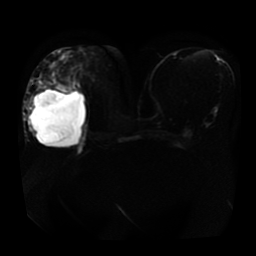
Breast MRI, one axial slice; position 21 of 41 along the scan axis; diffusion-weighted series; image 2 of 4 stored at this slice position (different b-values; order by instance number); 1.5 T; 5 mm slice thickness; 256 × 256 image matrix, field of view 360 × 360 mm. Female patient.
Outlined on this slice (manually delineated by an expert):
- tumour on diffusion-weighted imaging: bounding box <54,85,75,94> (left, top, right, bottom; pixels)